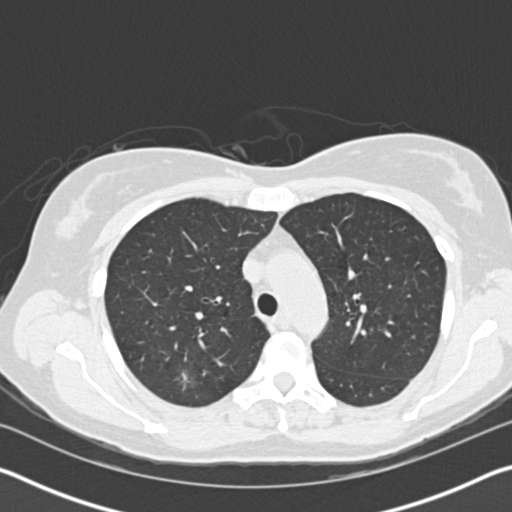
Low-dose screening chest CT, axial slice; first (baseline) screen; lung window (W 1500 / L -600 HU); 2 mm slice thickness; standard (soft-tissue) reconstruction kernel (B30f); slice 47 of 150 in the series. Female participant, aged 58 years at enrolment. Current smoker at enrolment.
Expert-annotated lung lesion, box from (x=158, y=356) to (x=212, y=406) px. The screening reader recorded 3 non-calcified nodules or masses ≥4 mm on this exam (right upper lobe, left upper lobe, left upper lobe); which of them this box marks is not recorded. Official screen result: positive, change unspecified: nodule(s) >= 4 mm or enlarging nodule(s), mass(es), or other non-specific abnormalities suspicious for lung cancer. Participant outcome: lung cancer diagnosed 487 days after this screen — bronchiolo-alveolar adenocarcinoma, NOS, right upper lobe, moderately differentiated (G2), stage IA (AJCC 6th edition), 7 mm at pathology.